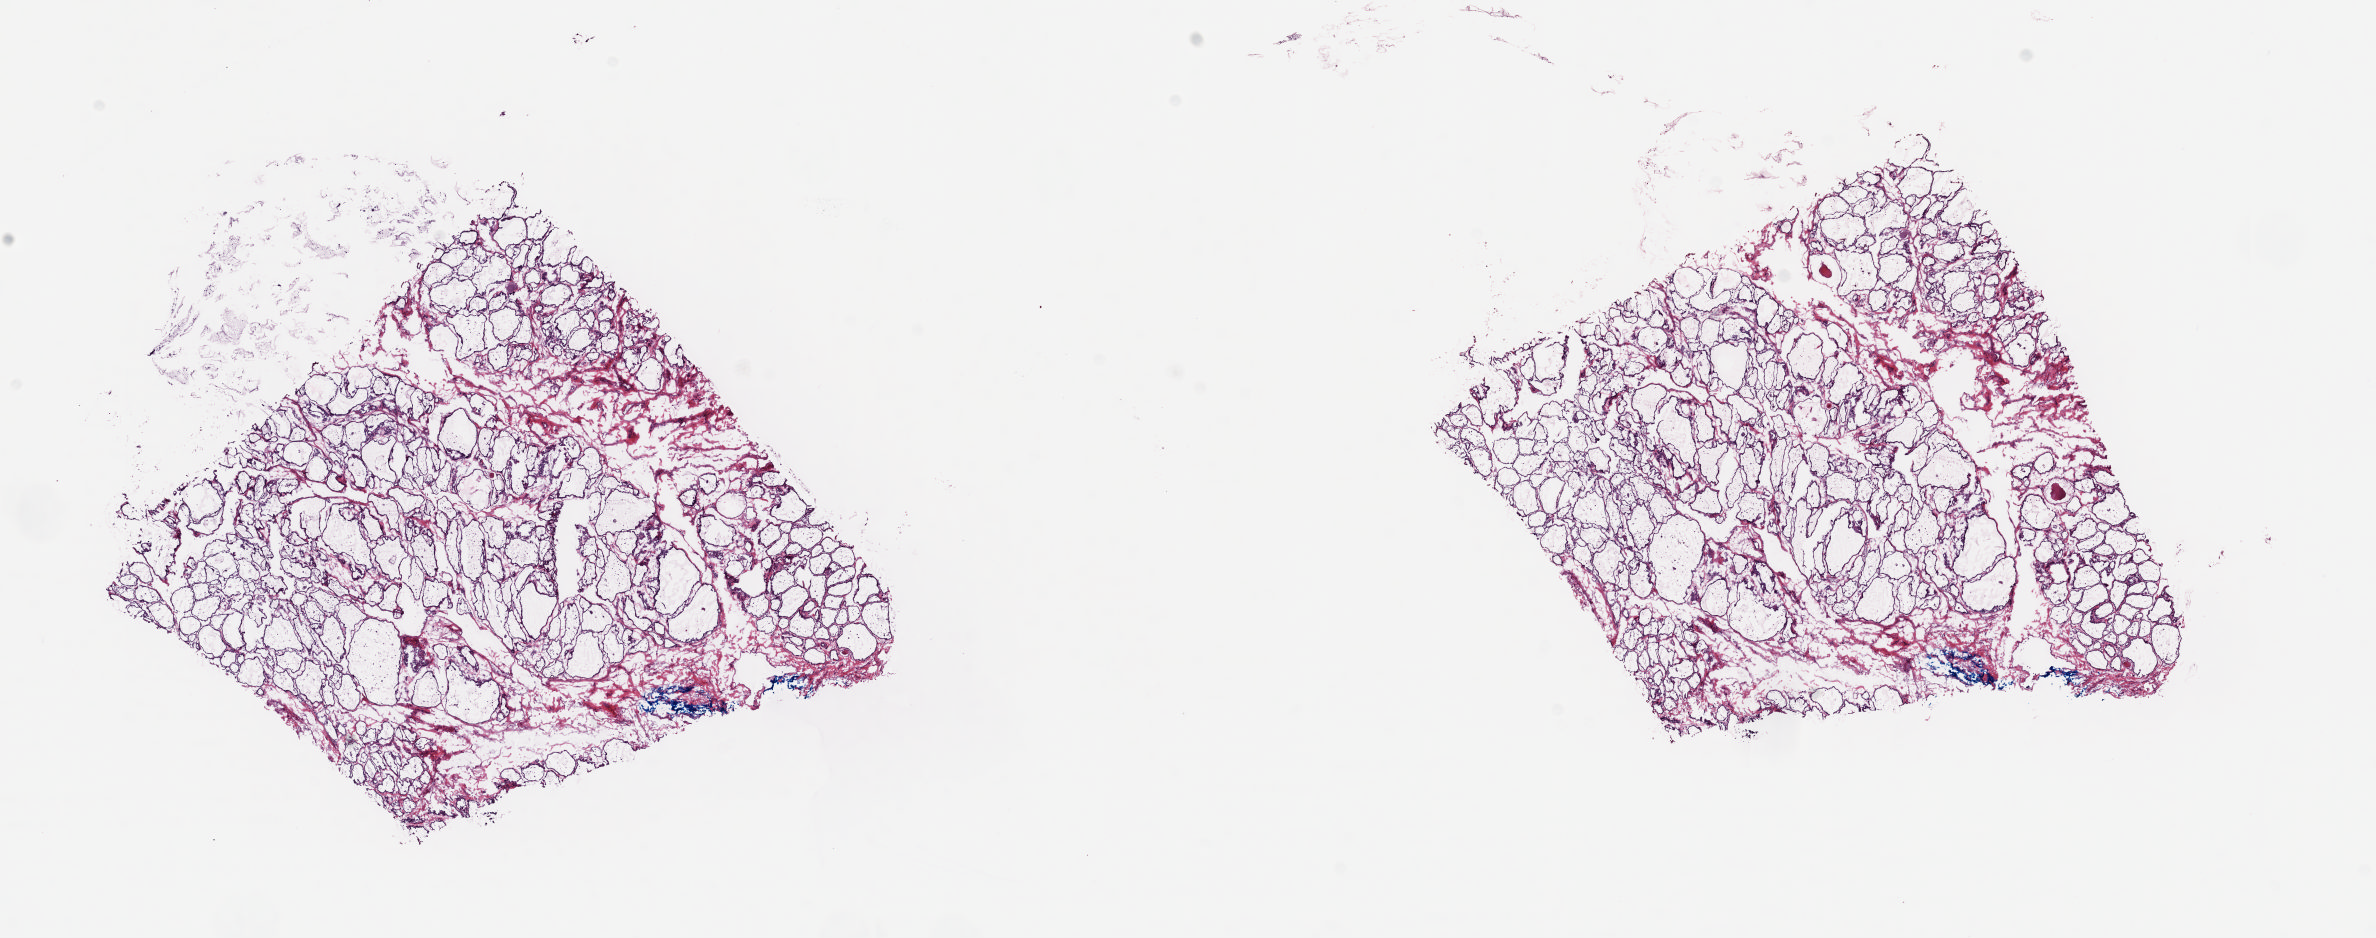
Digitized Hematoxylin and eosin (H&E) stained tissue section (whole slide), low-resolution overview of the scanned area, about 18.8 x 7.4 mm (slide scanned at 20x), frozen section from the top of the tissue portion, thyroid, solid tissue normal (non-tumour tissue) sample. Male, age 70 years at initial diagnosis. Slide review estimates, as recorded: tumour cells 0%, tumour nuclei 0%.
This section: solid tissue normal (non-tumour) sample from the same patient. Patient diagnosis: Papillary carcinoma, columnar cell (thyroid gland).